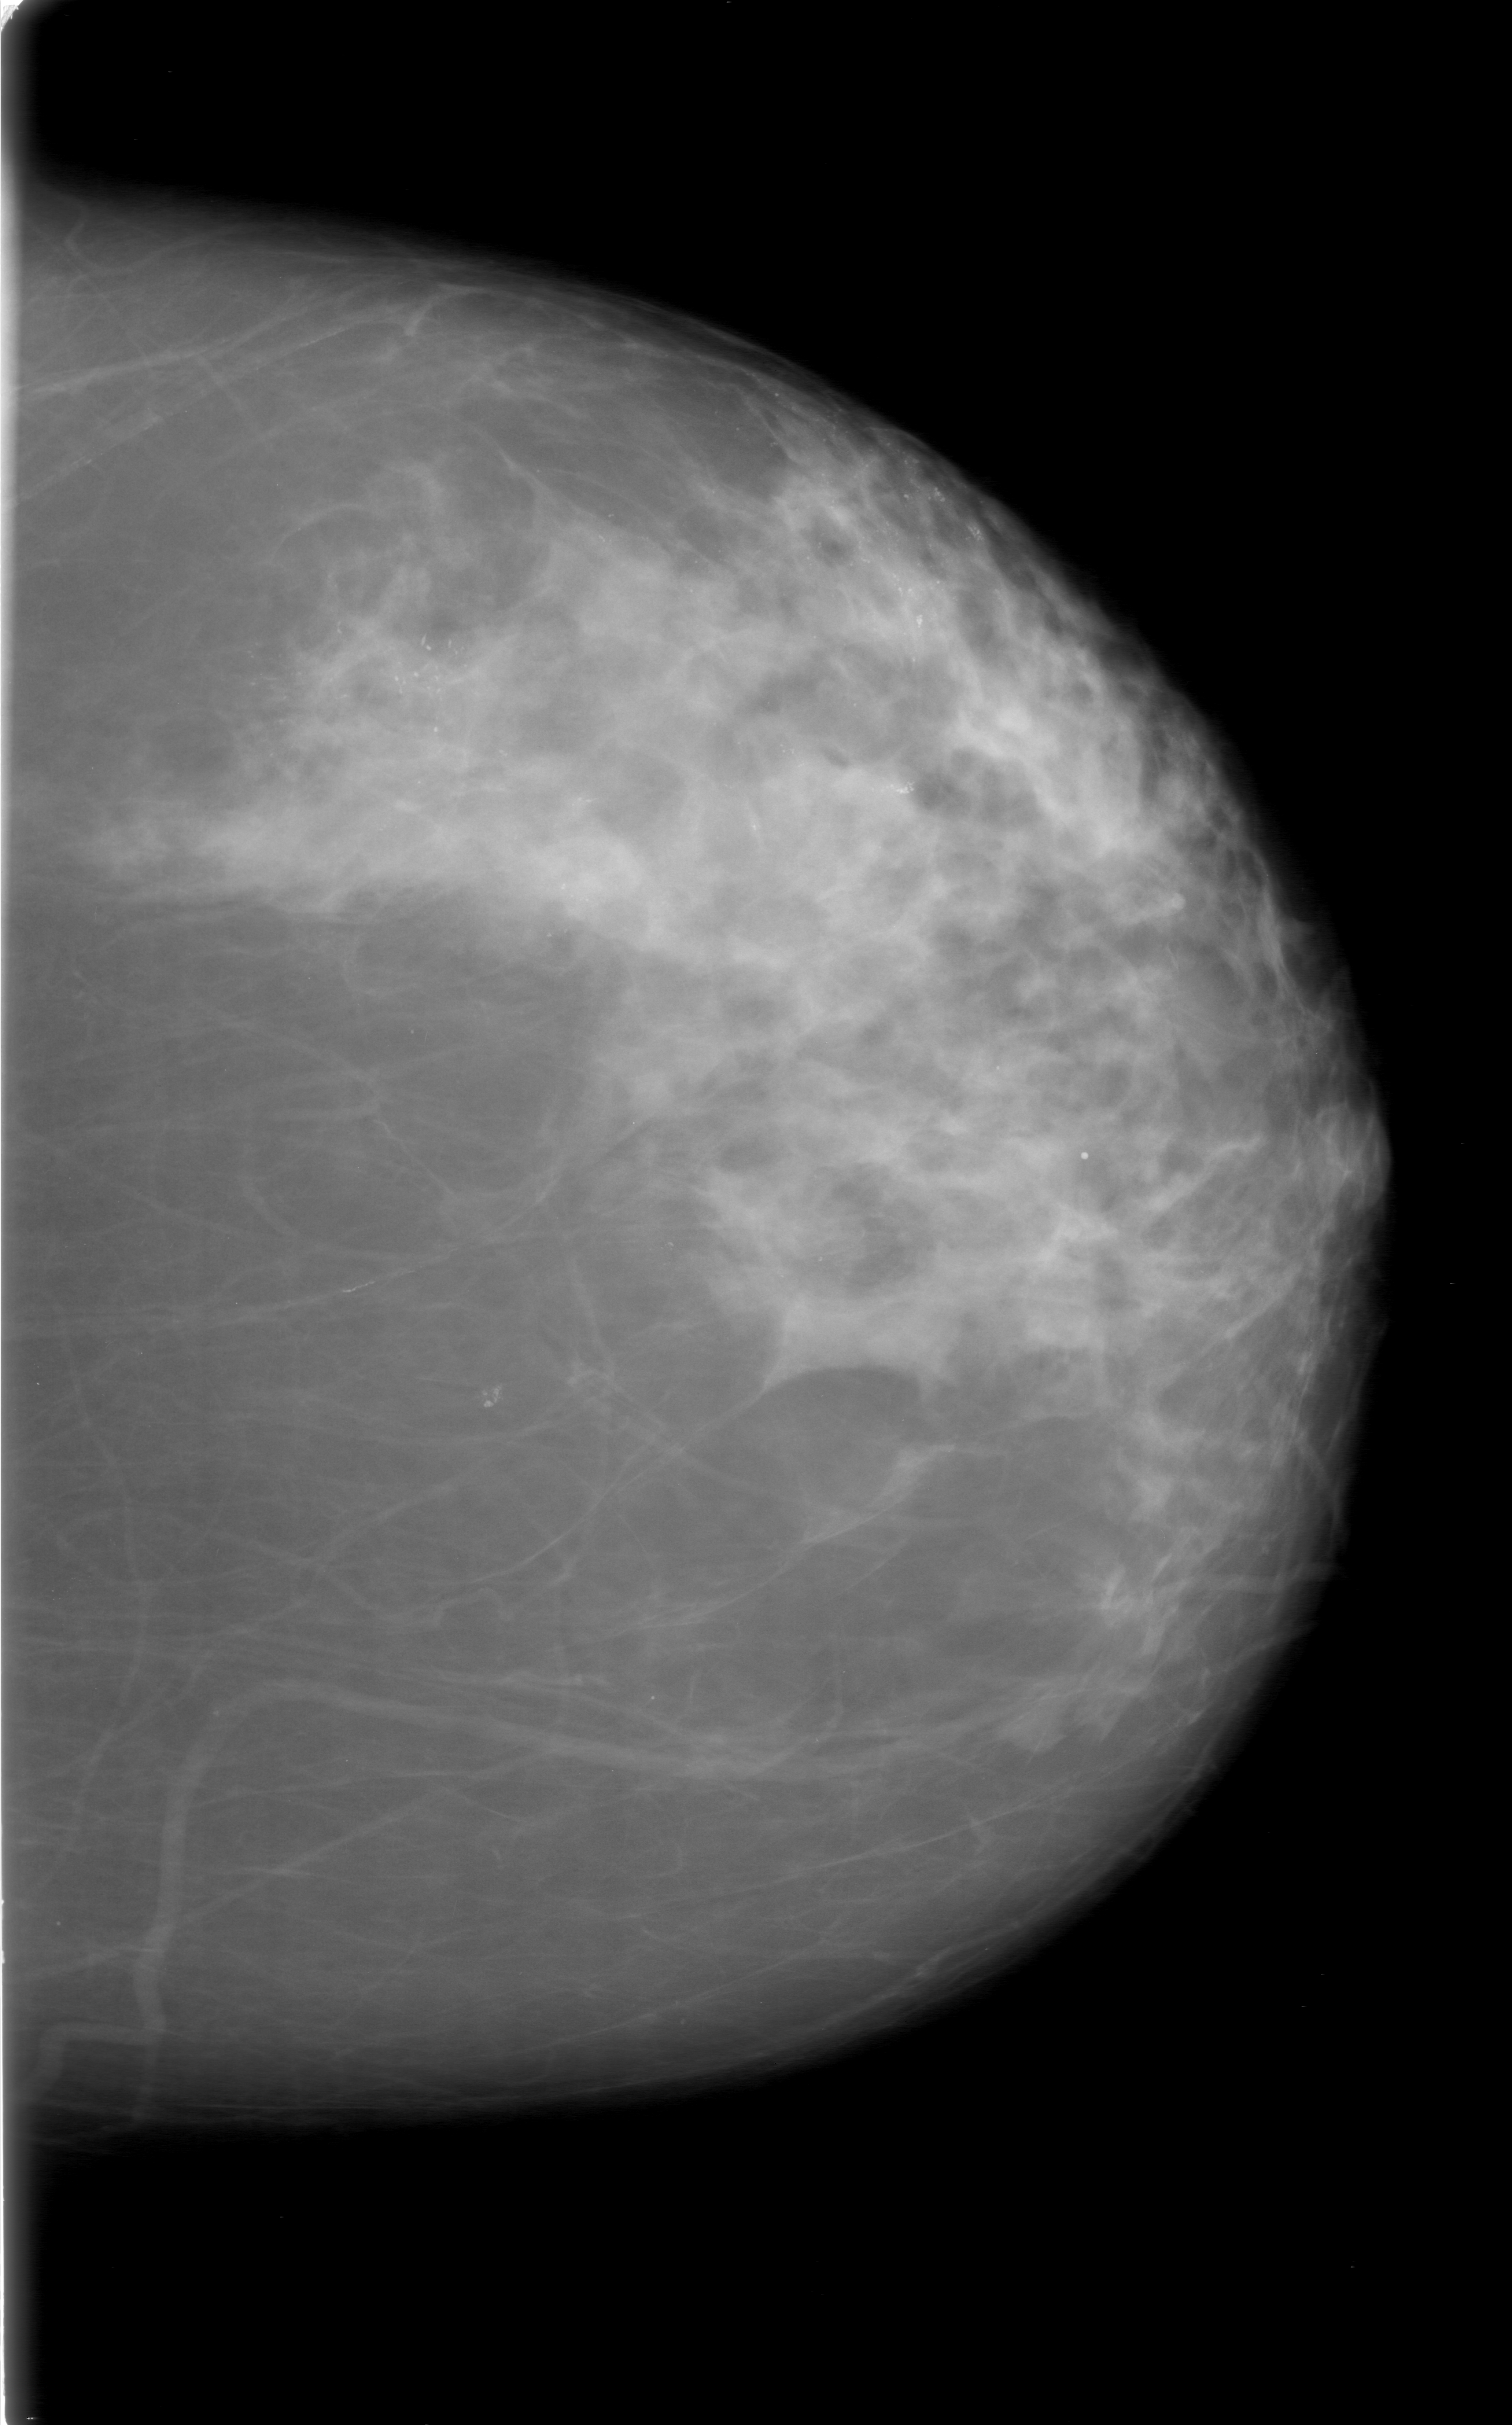
Digitized screen-film mammogram; left breast; craniocaudal (CC) view; BI-RADS breast density category 3 (scale 1–4).
Marked abnormality: calcifications, morphology pleomorphic, distribution regional; BI-RADS assessment category 5; subtlety rating 5 on a 1 (subtle) to 5 (obvious) scale; pathology result (as recorded, not read from the image): malignant.